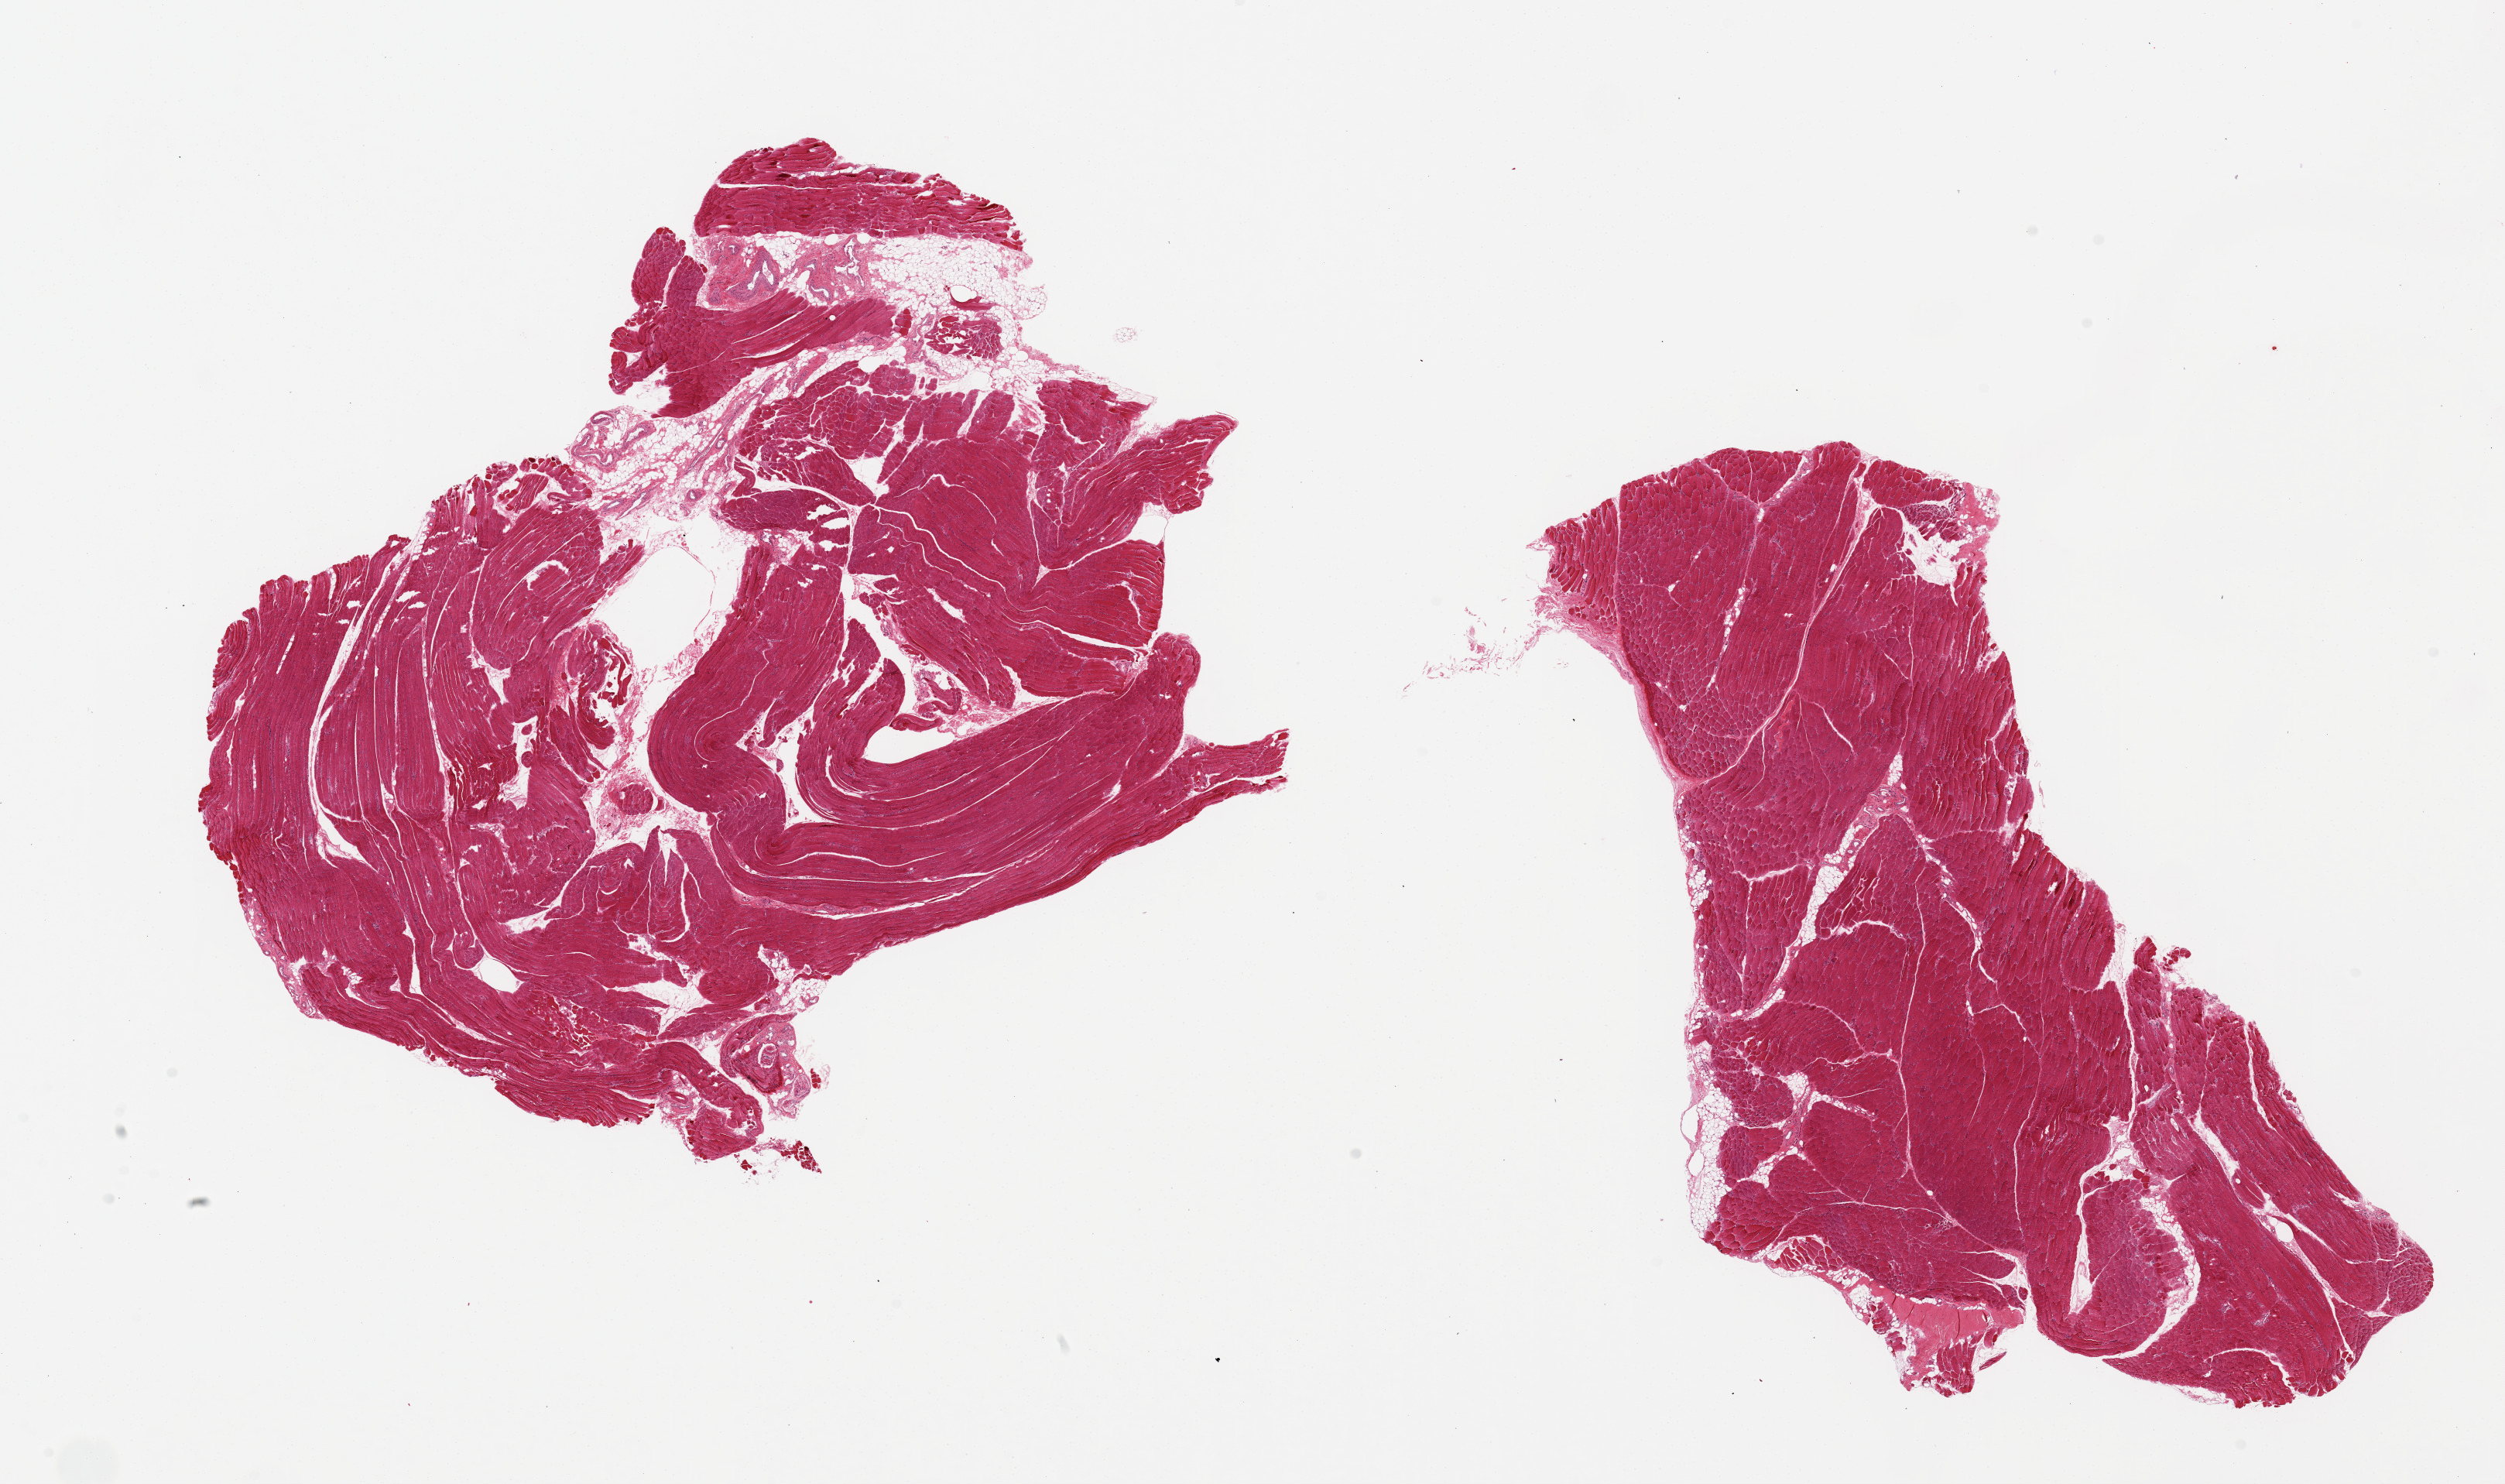
Haematoxylin and eosin whole-slide image, shown as a low-resolution overview of the whole scanned area (about 25.6 x 15.2 mm), PAXgene-fixed, paraffin-embedded tissue, section of skeletal muscle (target tissue), donor tissue sample. Donor sex: female.
Pathologist's review note for this sample: 2 pieces, 11x8 & 11x6mm; <5% internal adipose.